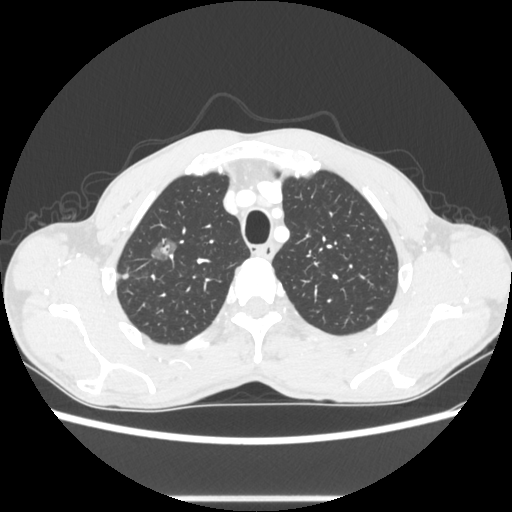
Chest CT, one axial slice; position 233 of 289 along the scan axis; reconstruction kernel STANDARD; 100 kVp; lung window (W 1500 / L -600 HU); 1.25 mm slice thickness; 512 × 512 image matrix, field of view 350 × 350 mm. Patient: male, 54 years. From the clinical record (not read from this slice): clinical TNM (as recorded): T1a N0 M0.
Outlined on this slice (rectangle marked by the reading radiologist):
- lung tumour (recorded histology: adenocarcinoma): bounding box (x1, y1, x2, y2) in pixels: (143, 230, 179, 263)